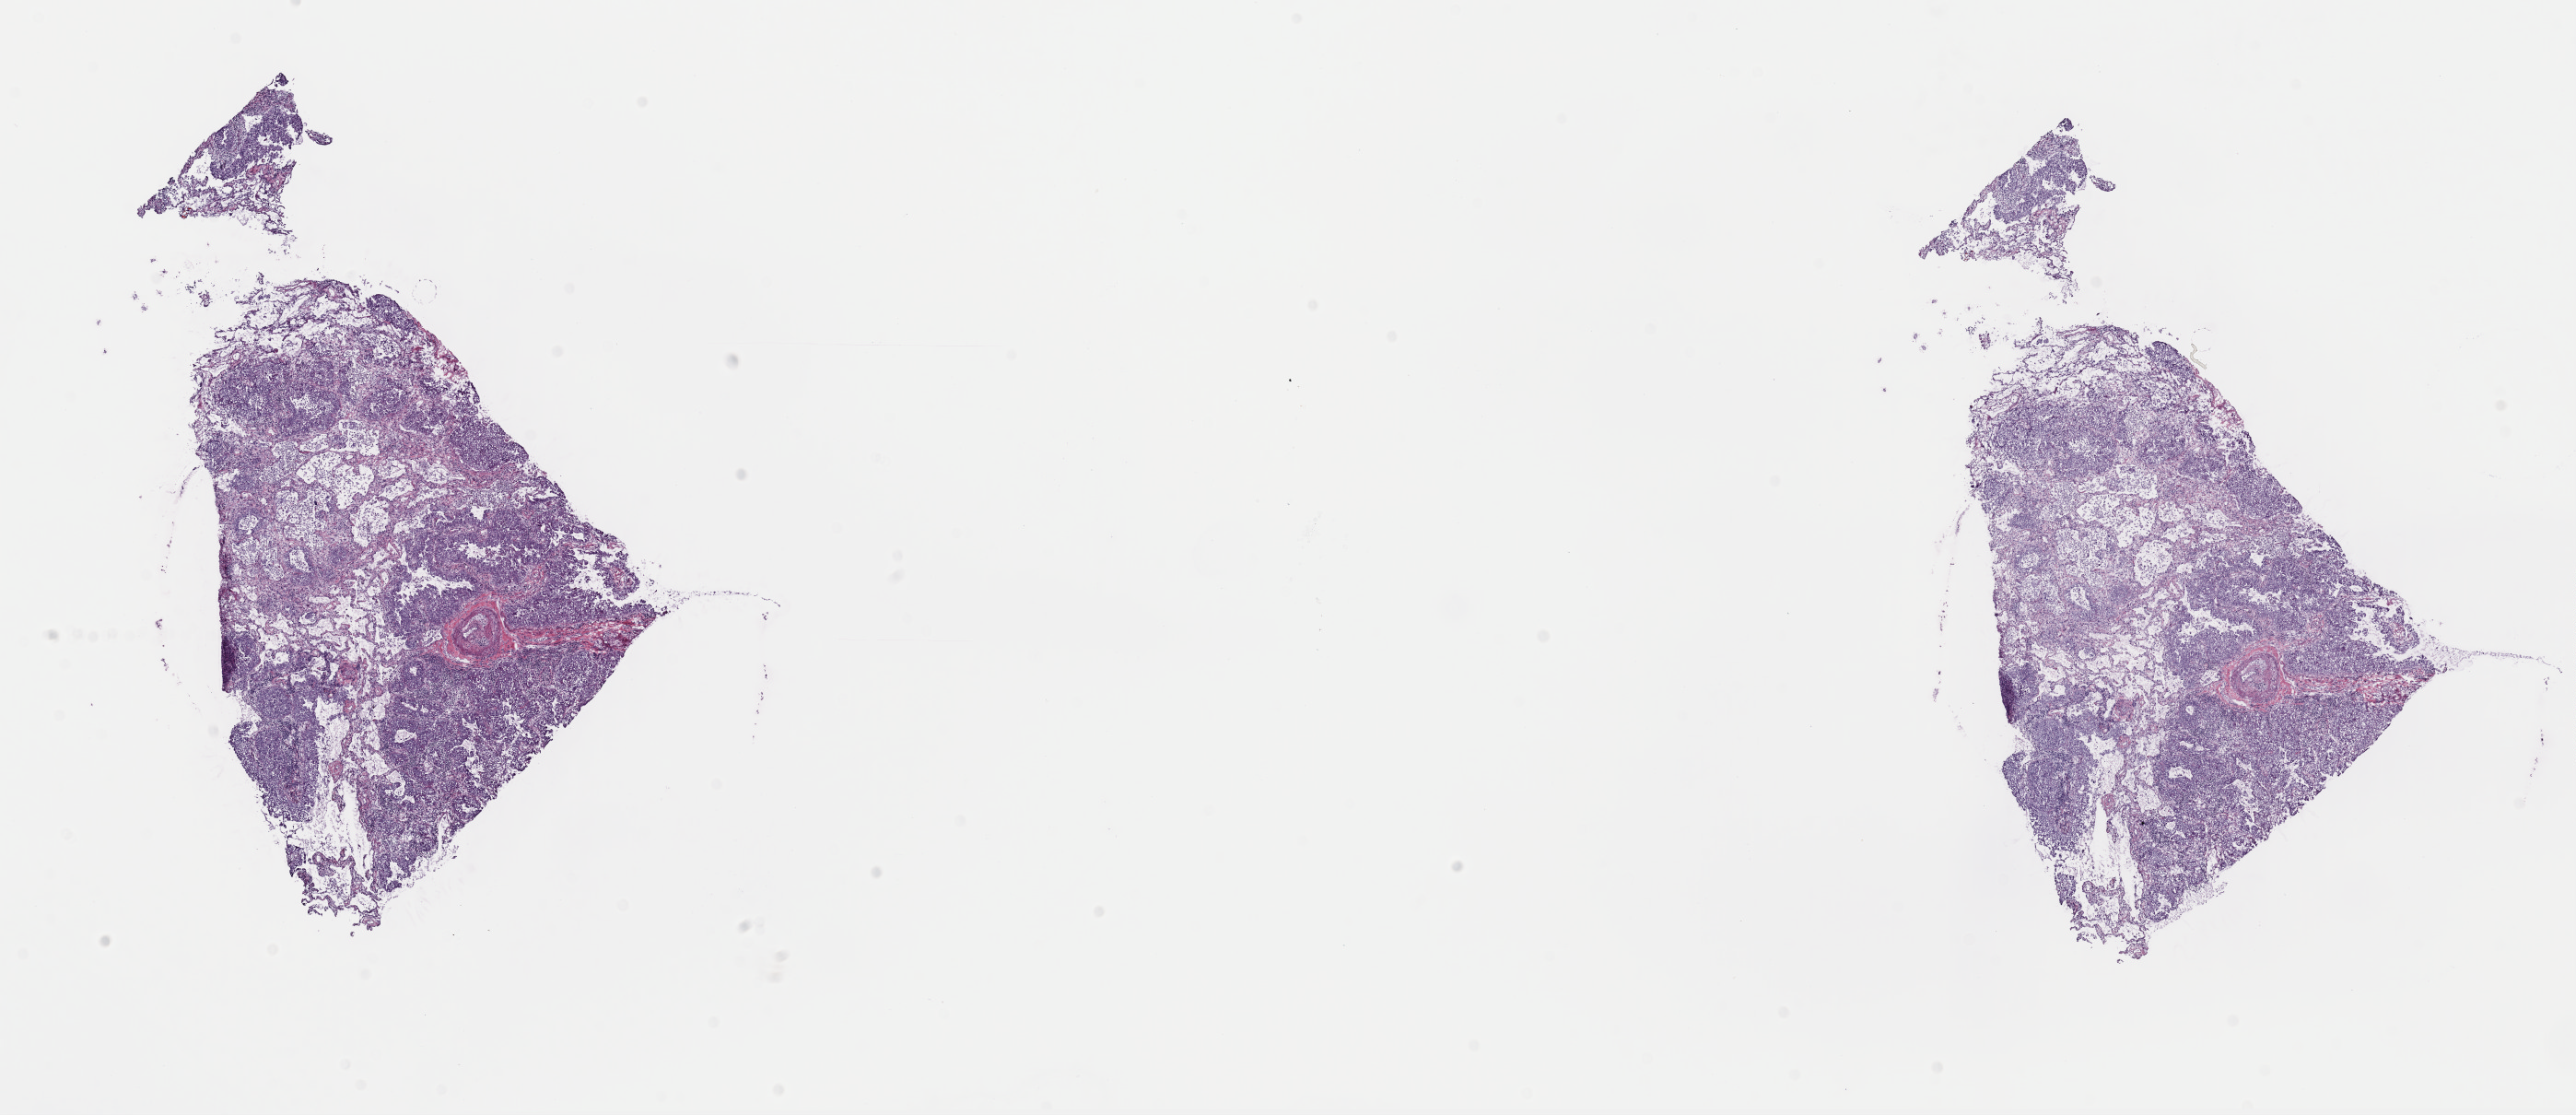
Whole-slide histology image, H&E — whole scanned area (about 22.1 x 9.6 mm) shown as a low-resolution overview, frozen section from the top of the tissue portion, sample: primary tumour, lung. Male, age 73 years at initial diagnosis. Composition of this section per pathologist review: tumour cells 70%, tumour nuclei 70%.
Histologic diagnosis: Adenocarcinoma, NOS (upper lobe, lung).